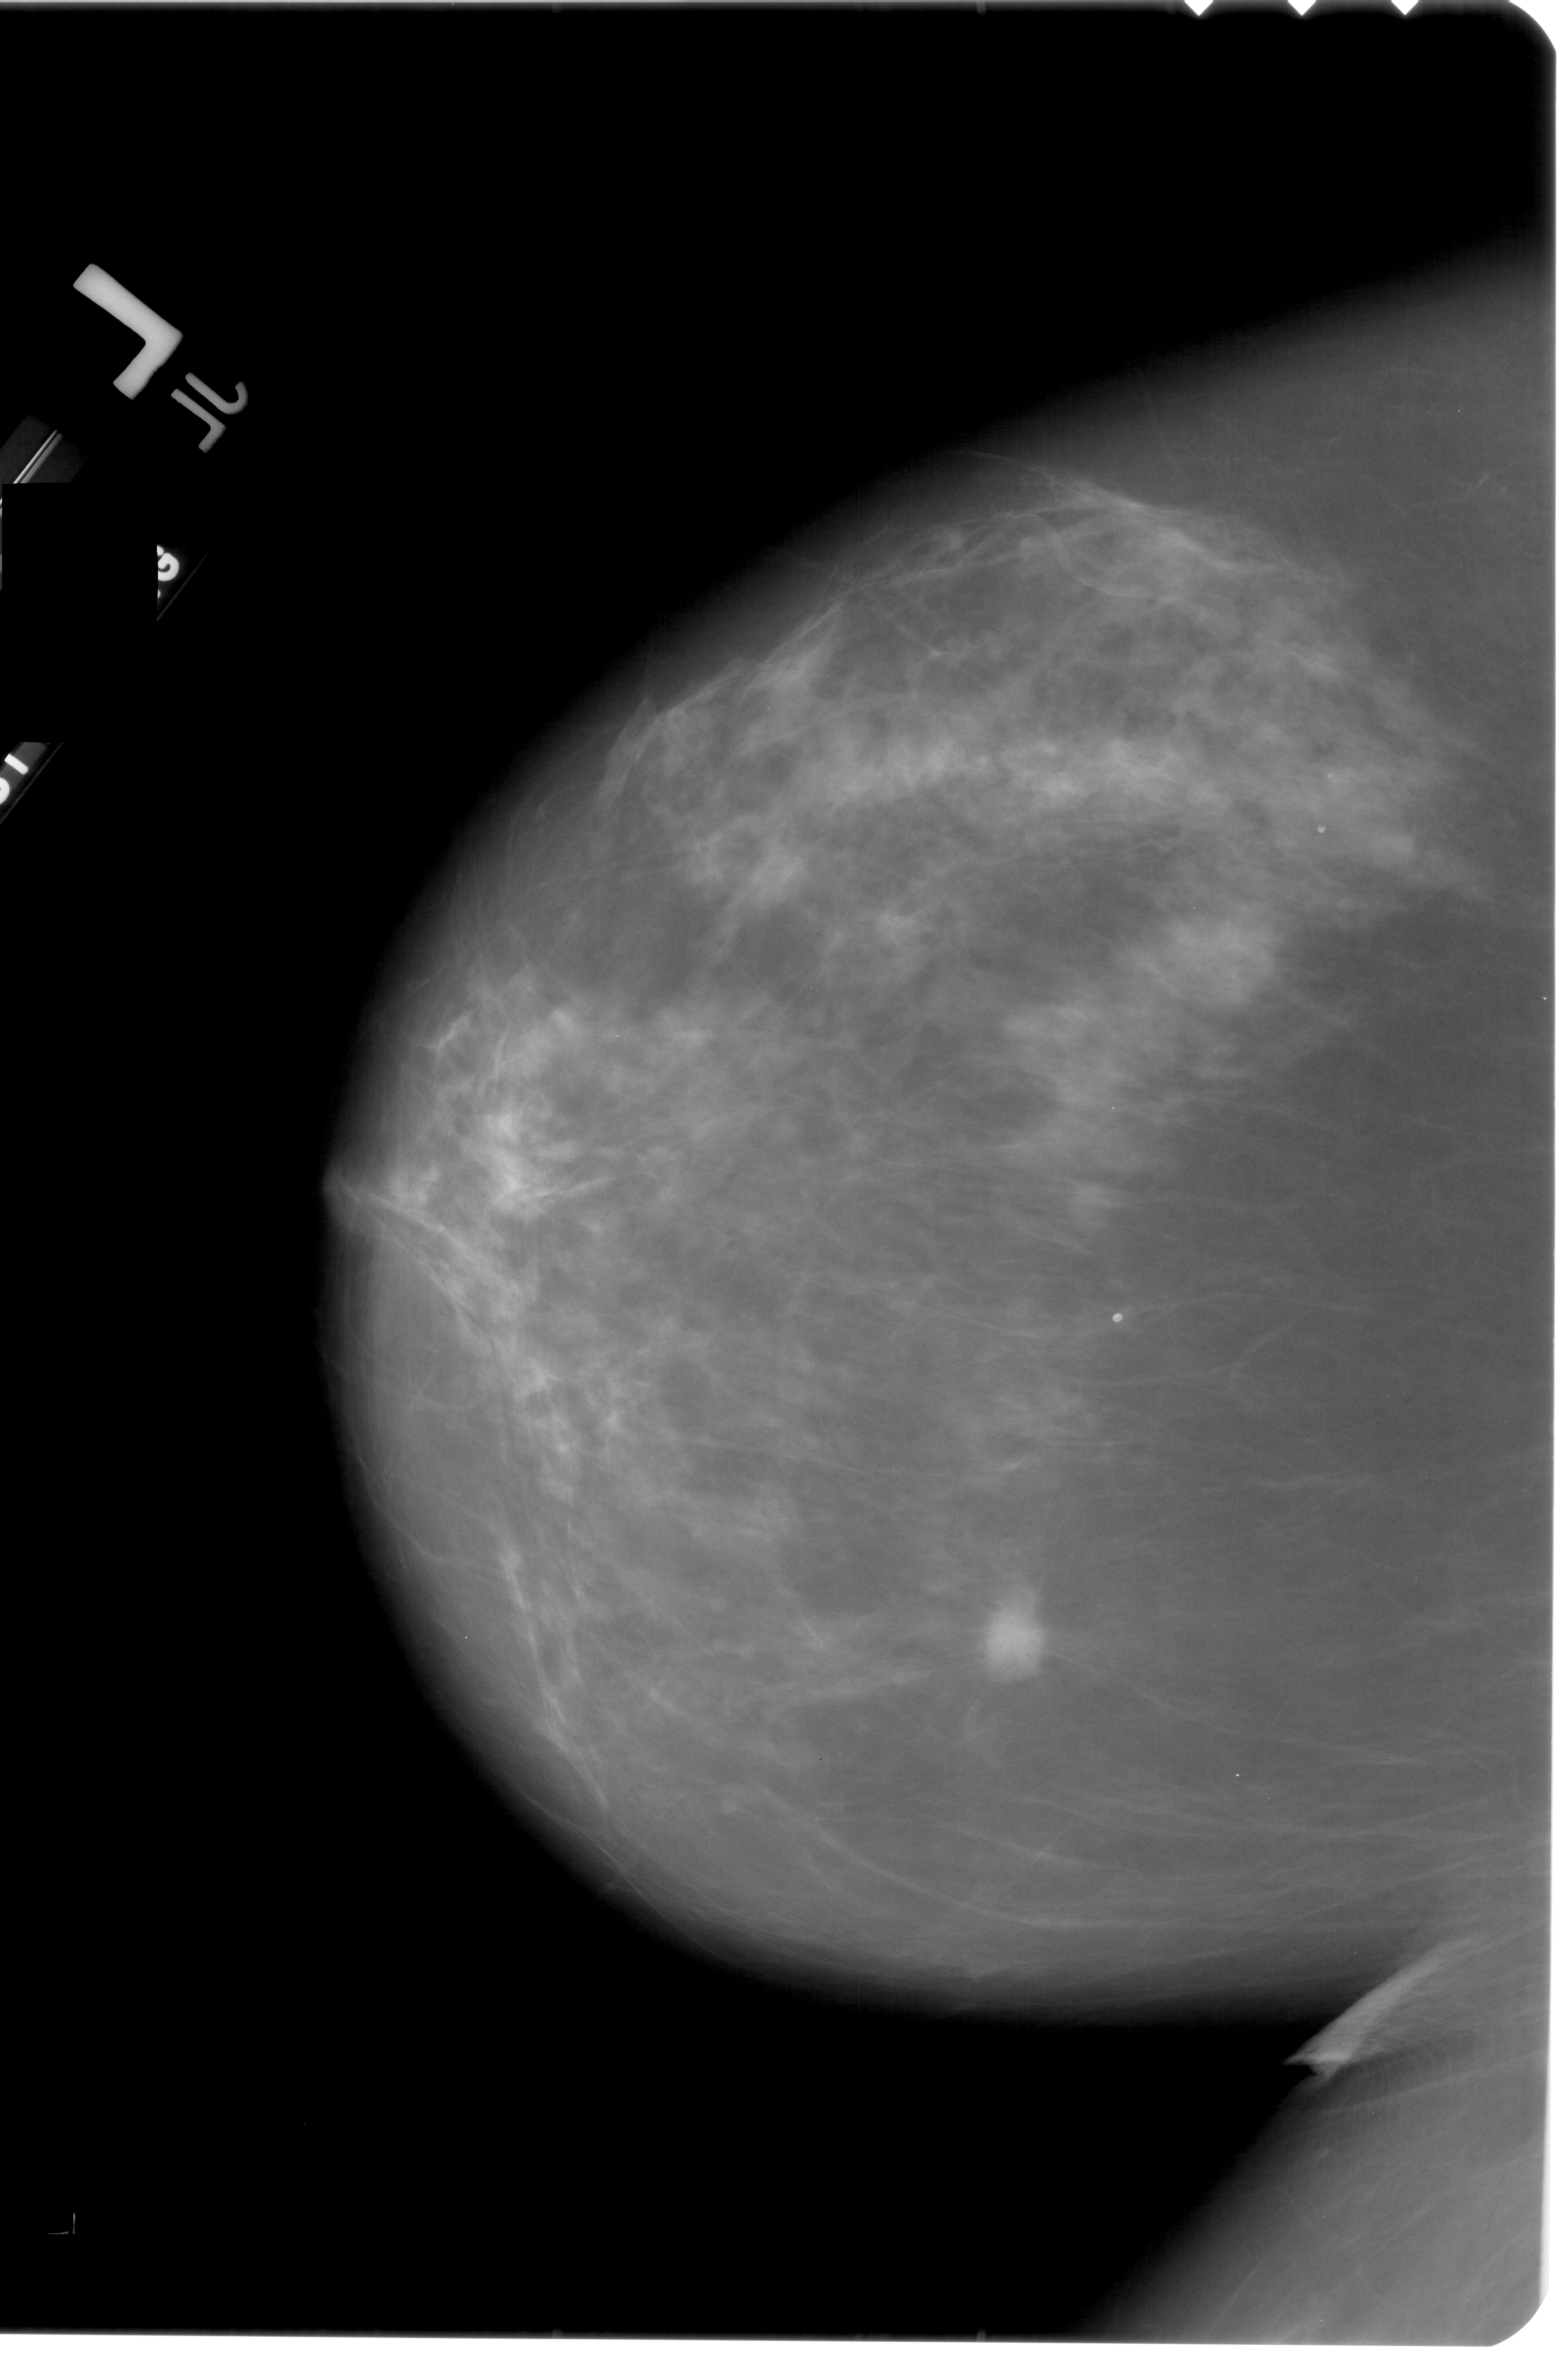
Mammogram (digitized film); left breast; craniocaudal (CC) view; 1559 × 2380 image matrix.
Expert-marked regions of interest on this image (one box per marked abnormality):
- mass, shape irregular, margins spiculated; BI-RADS assessment category 5; subtlety rating 5 on a 1 (subtle) to 5 (obvious) scale; pathology result (as recorded, not read from the image): malignant: bounding box [x1, y1, x2, y2] px = [966, 1577, 1066, 1687]